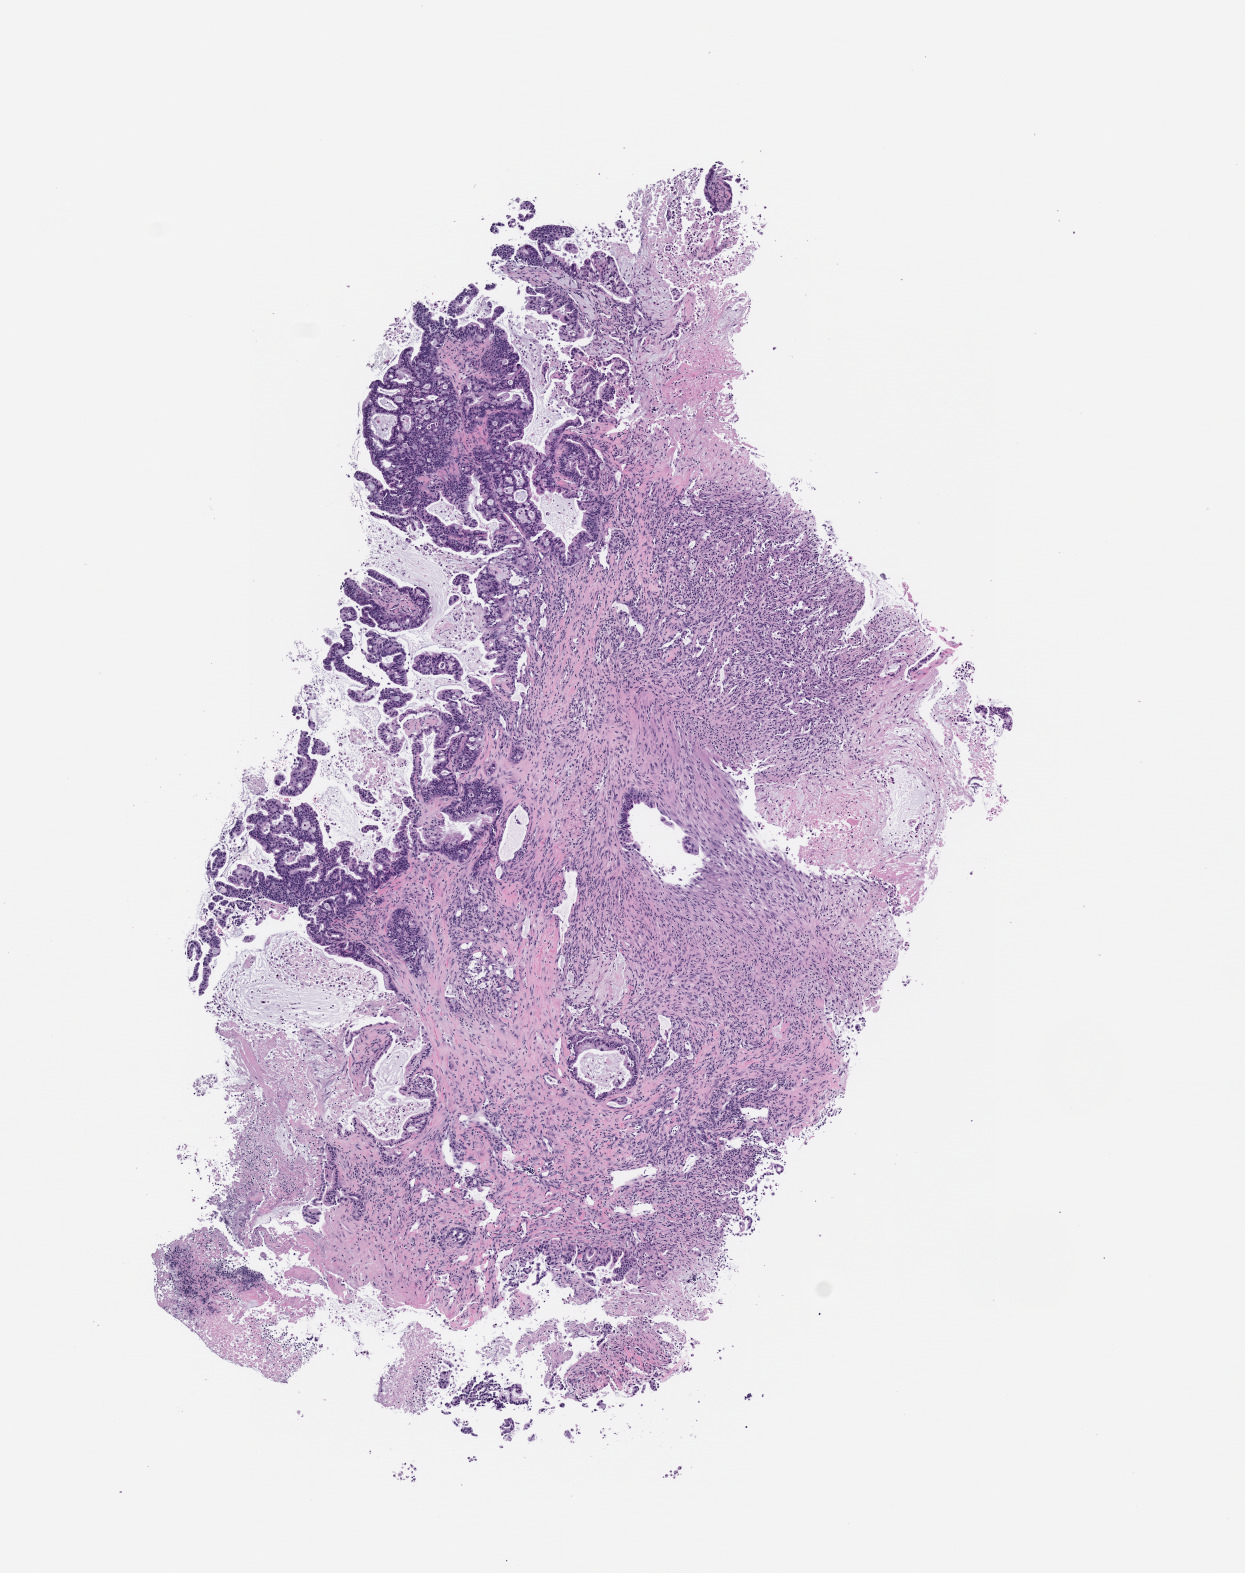
Haematoxylin and eosin whole-slide image of a patient-derived xenograft (PDX) tumor grown in a mouse, a low-resolution overview of the entire scanned area, about 5.0 x 6.3 mm. Formalin-fixed paraffin-embedded section. Originating tumor site category: small intestine.
Originating patient diagnosis: Small Intestinal Adenocarcinoma.